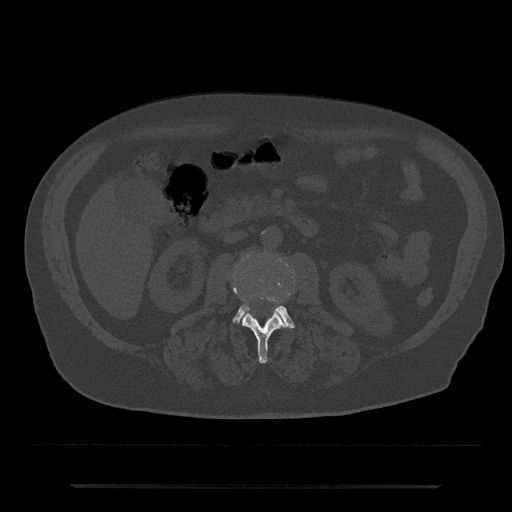
CT including the spine, one axial slice; slice 446 of 797 in the series (ordered by position); reconstruction kernel Br40s/3; 120 kVp; bone window (W 1800 / L 400 HU); 0.5 mm slice thickness; 512 × 512 image matrix, field of view 434 × 434 mm. Patient: male, 80 years. From the clinical record (not read from this slice): primary cancer: prostate; vertebrae with lytic lesions (as recorded): L1, T11.
Structures marked on this image (semi-automatically segmented with operator editing):
- L2 vertebra: bounding box [x1, y1, x2, y2] px = [233, 287, 288, 364]
- L3 vertebra: [232, 305, 295, 329]